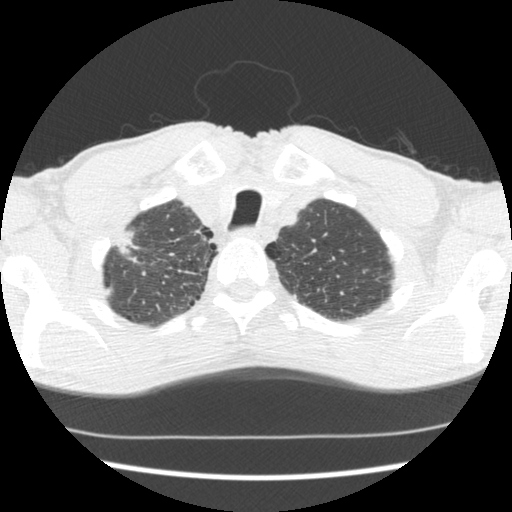
Low-dose screening chest CT, axial slice. First (baseline) screen. Lung window (W 1500 / L -600 HU). Standard (soft-tissue) reconstruction kernel (STANDARD). Slice 30 of 197 in the series. 512 × 512 image matrix, field of view 318 × 318 mm. Male, age 62 years at enrolment.
• Expert reader's lesion annotation, bounding box [x1, y1, x2, y2] px = [98, 225, 148, 273].
• Screening reader's record for this exam: no non-calcified nodule ≥4 mm recorded.
• Official screen result: negative screen, significant abnormalities not suspicious for lung cancer.
• Participant outcome: lung cancer diagnosed 640 days after this screen — adenocarcinoma, NOS, right upper lobe, poorly differentiated (G3), stage IIA (AJCC 6th edition), 22 mm at pathology.